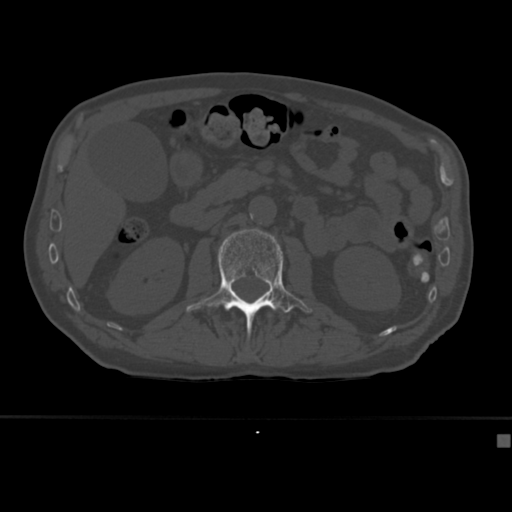
CT including the spine, one axial slice. Position 150 of 430 along the scan axis. 120 kVp. Bone window (W 1800 / L 400 HU). 1.5 mm slice thickness. 512 × 512 image matrix, field of view 337 × 337 mm. Male patient, age 64 years. Case-level facts recorded for this patient, not image findings: primary cancer: uterus.
Structures marked on this image (semi-automatically segmented with operator editing):
- L1 vertebra: bounding box <233,310,275,318> (left, top, right, bottom; pixels)
- L2 vertebra: <186,229,312,337>